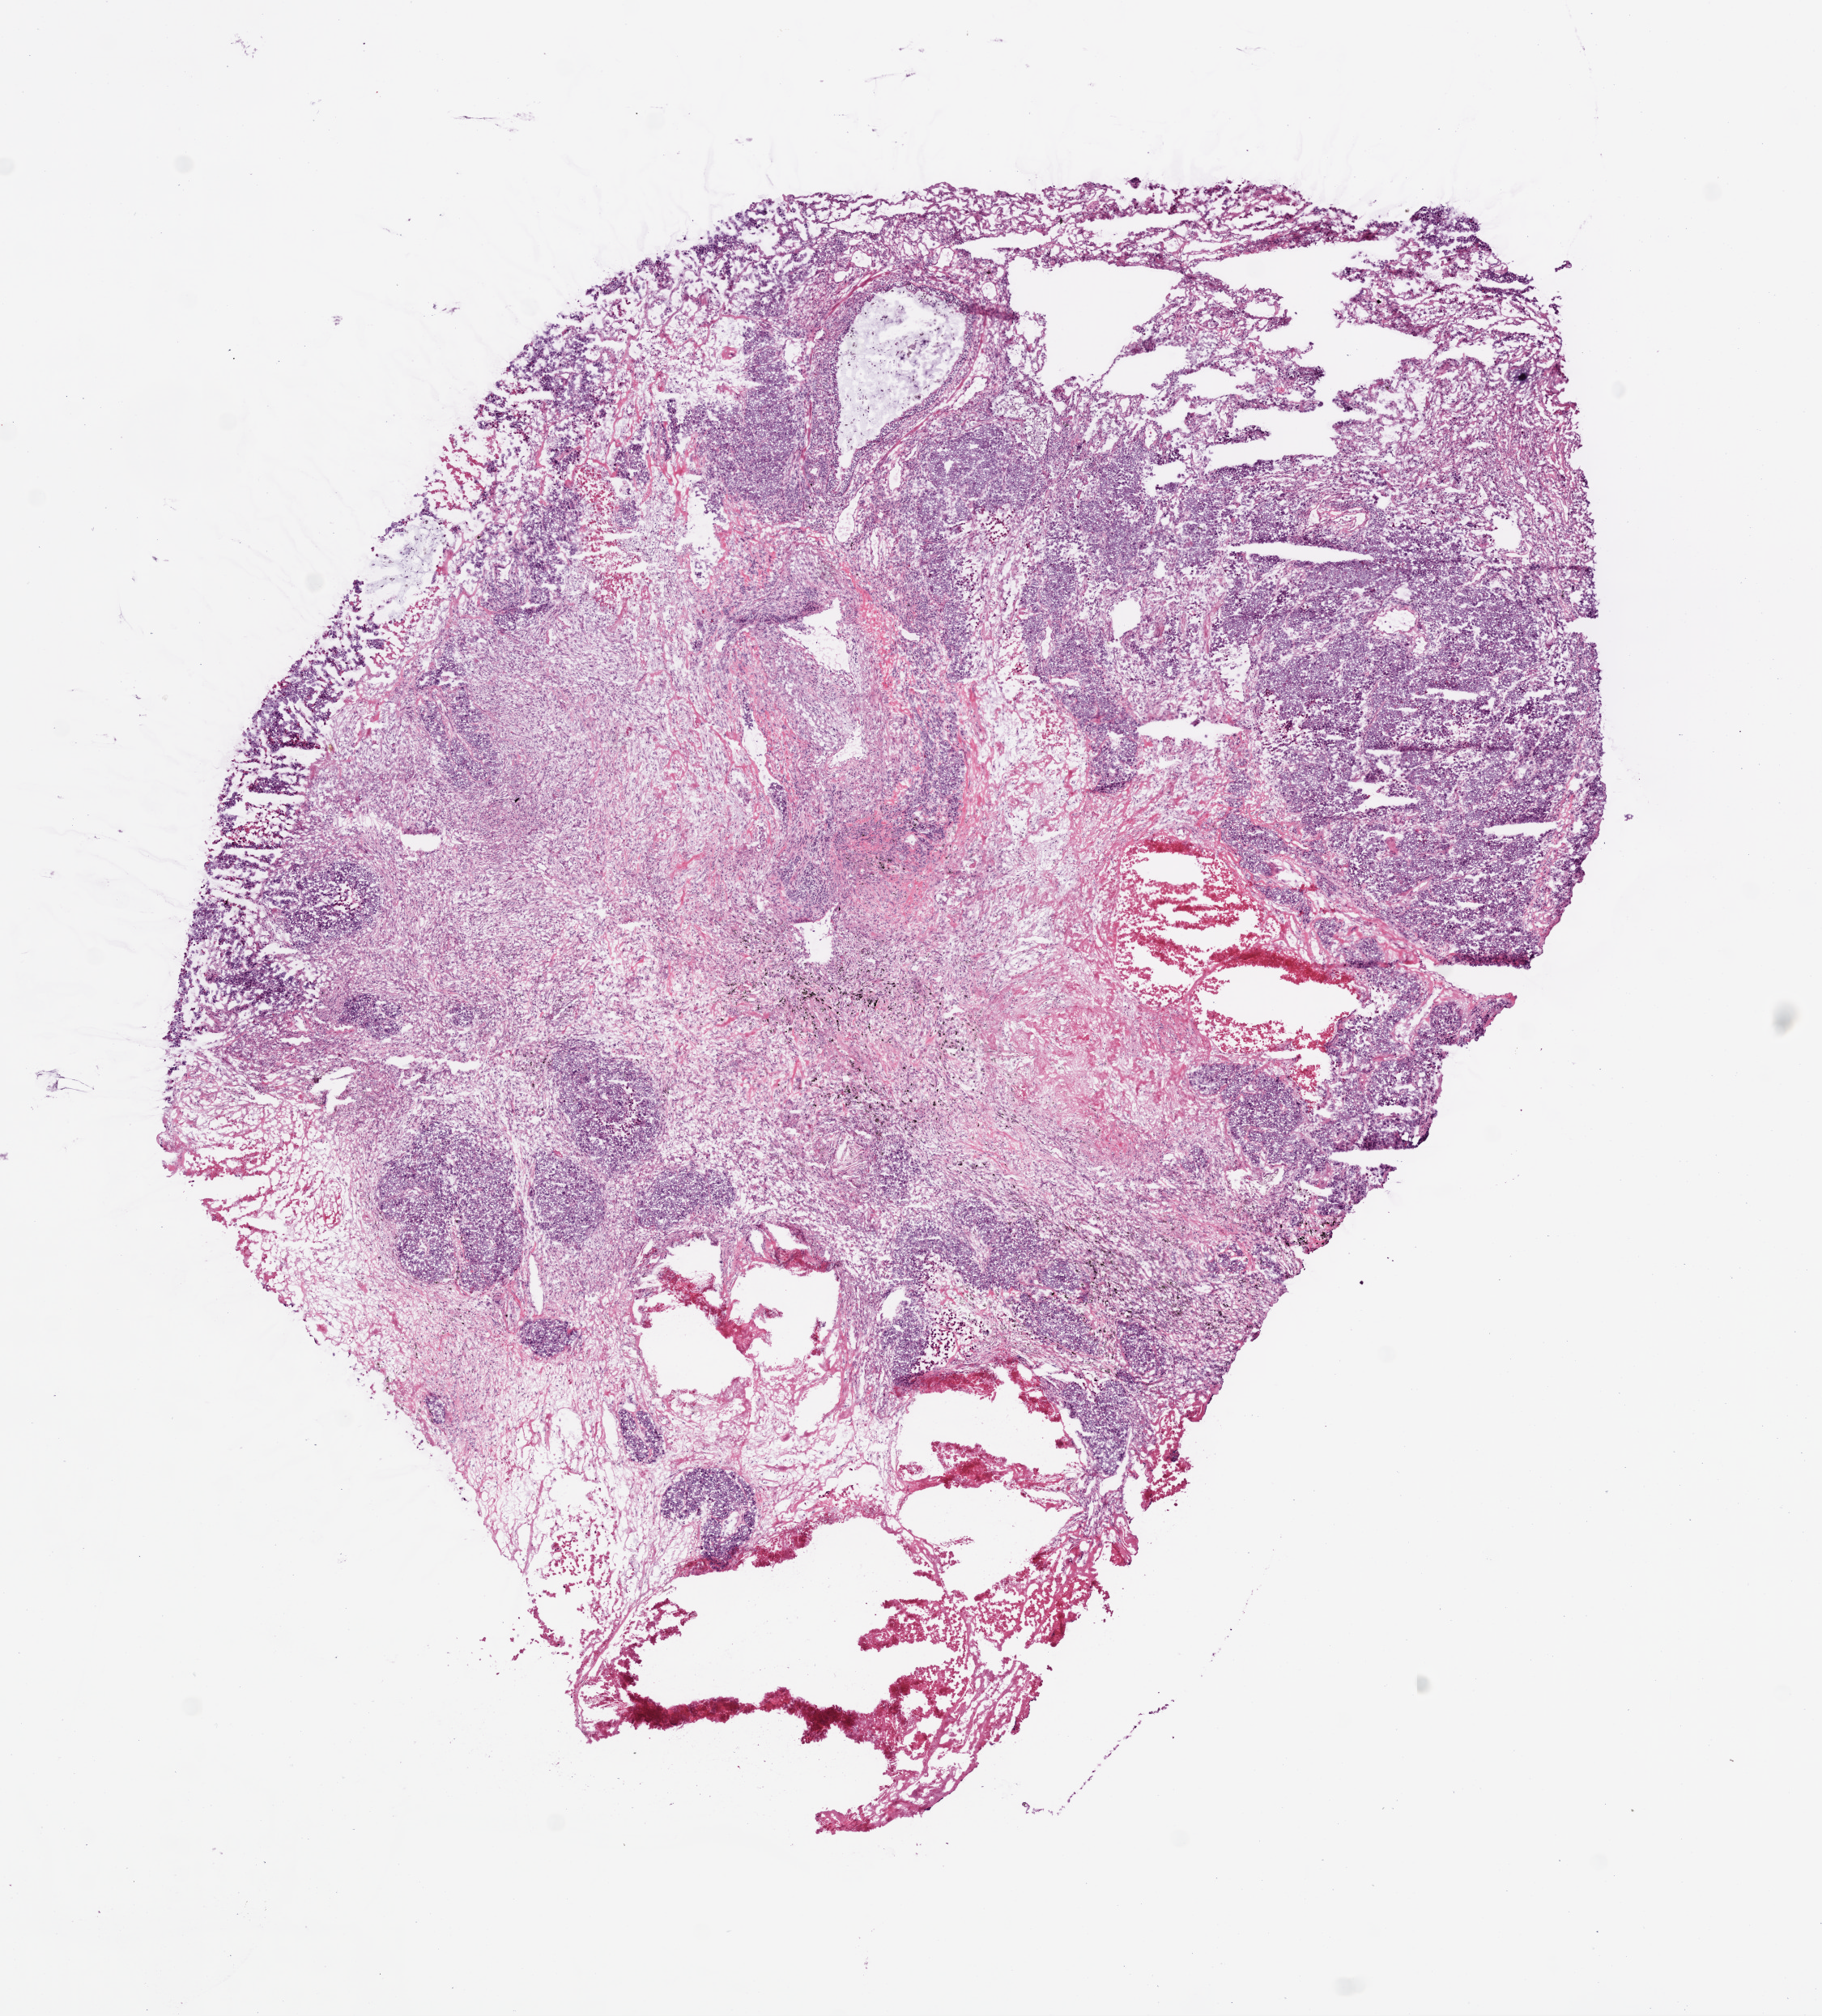
Digitized Hematoxylin and eosin (H&E) stained tissue section (whole slide), shown as a low-resolution overview of the whole scanned area (about 9.0 x 10.0 mm), frozen section, lung, primary tumour sample. Patient: male, age at initial diagnosis 81 years. Slide review estimates, as recorded: tumour cells 50%, tumour nuclei 65%, normal cells 10%, stromal cells 25%, necrosis 15%. Inflammatory infiltration, as recorded: lymphocyte infiltration 2%.
AJCC pathologic stage: IIIA. TNM: T2 N2 M0. Histologic diagnosis: Adenocarcinoma, NOS (upper lobe, lung).